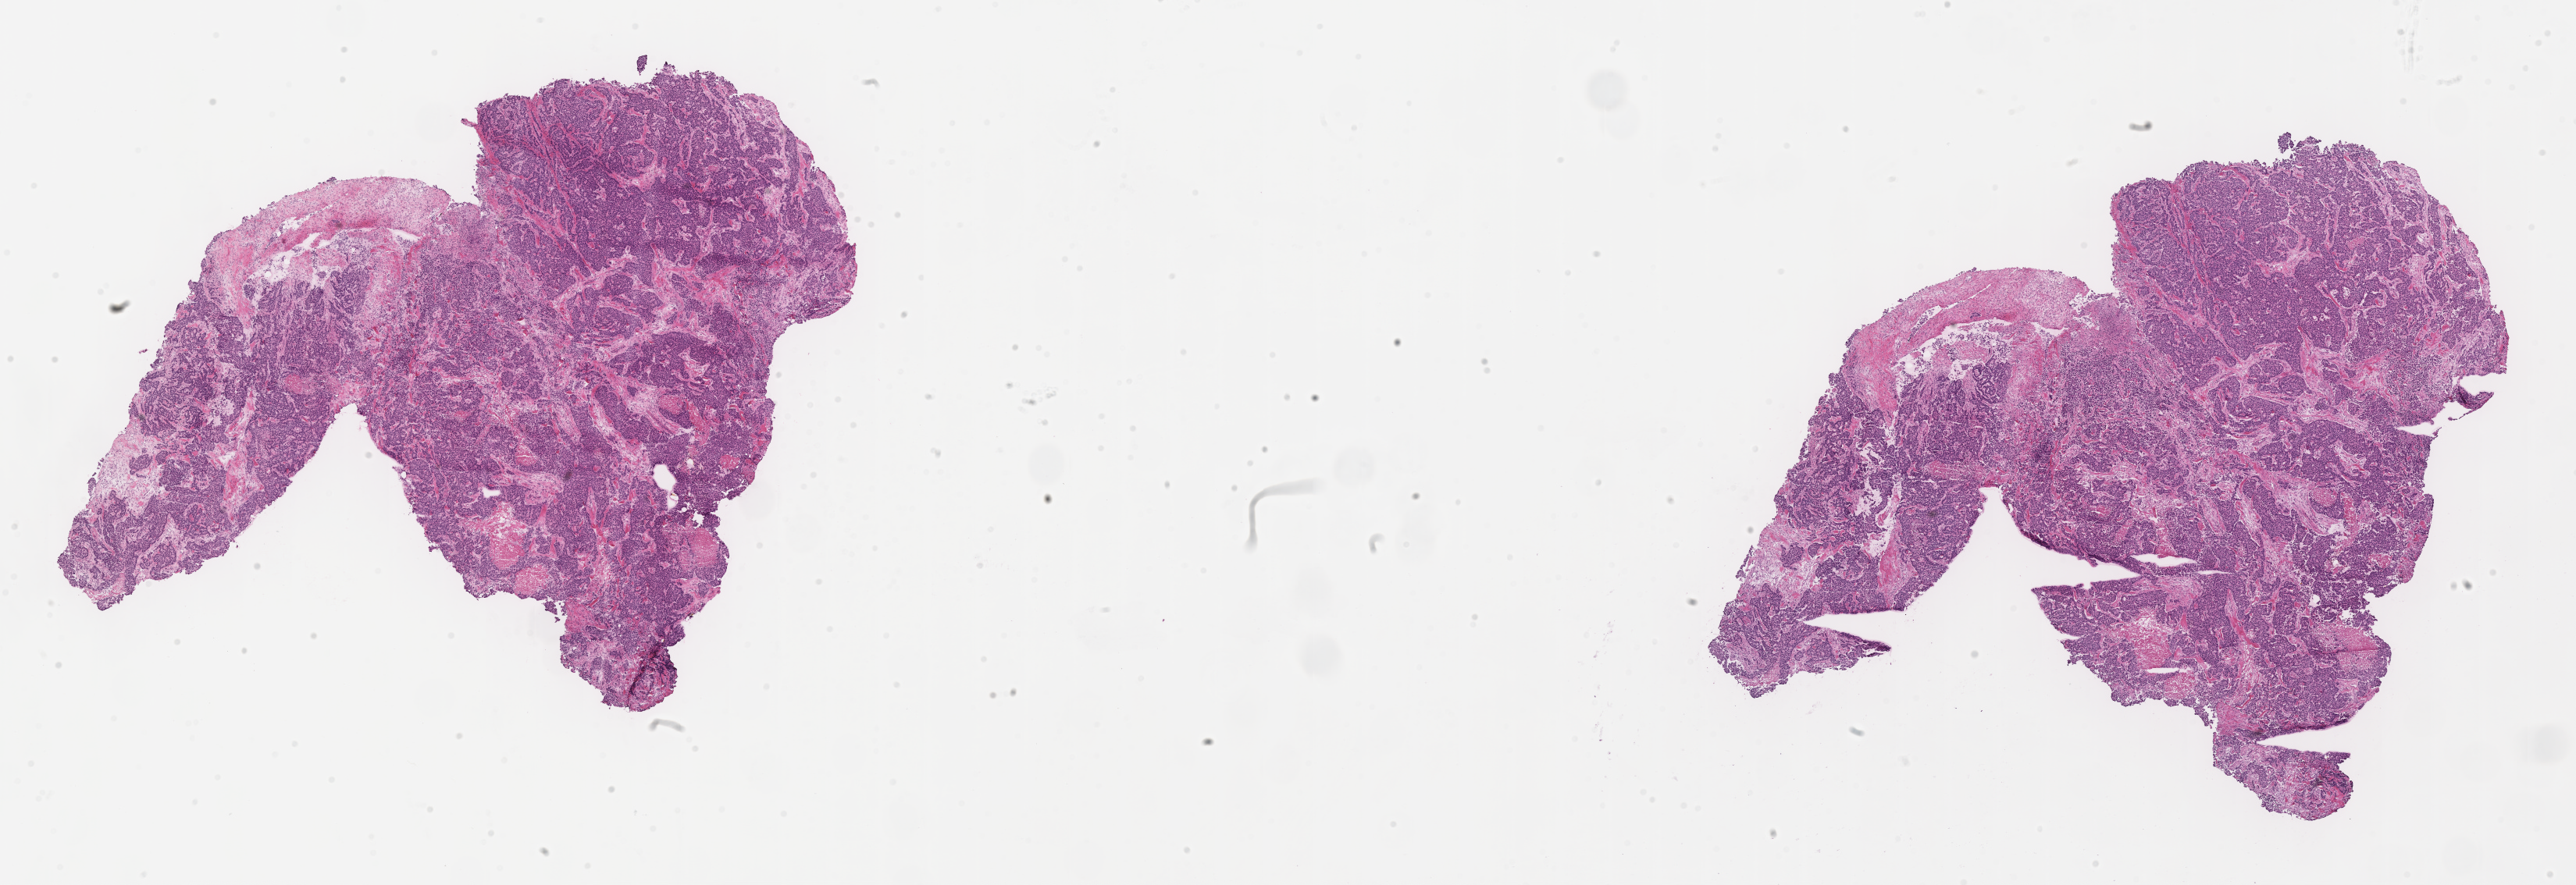
Digitized haematoxylin and eosin-stained section, shown as a low-resolution overview of the whole scanned area (about 26.6 x 9.1 mm), cryosection, specimen: primary tumor, anatomic site: breast. Female patient; age at initial diagnosis 55 years. Composition of this section per pathologist review: tumor cells 85%, tumor nuclei 85%, stromal cells 10%, necrosis 0%, normal cells 5%. Inflammatory infiltration, as recorded: lymphocyte infiltration 5%, monocyte infiltration 0%, neutrophil infiltration 0%.
Diagnosis: Infiltrating duct carcinoma, NOS.